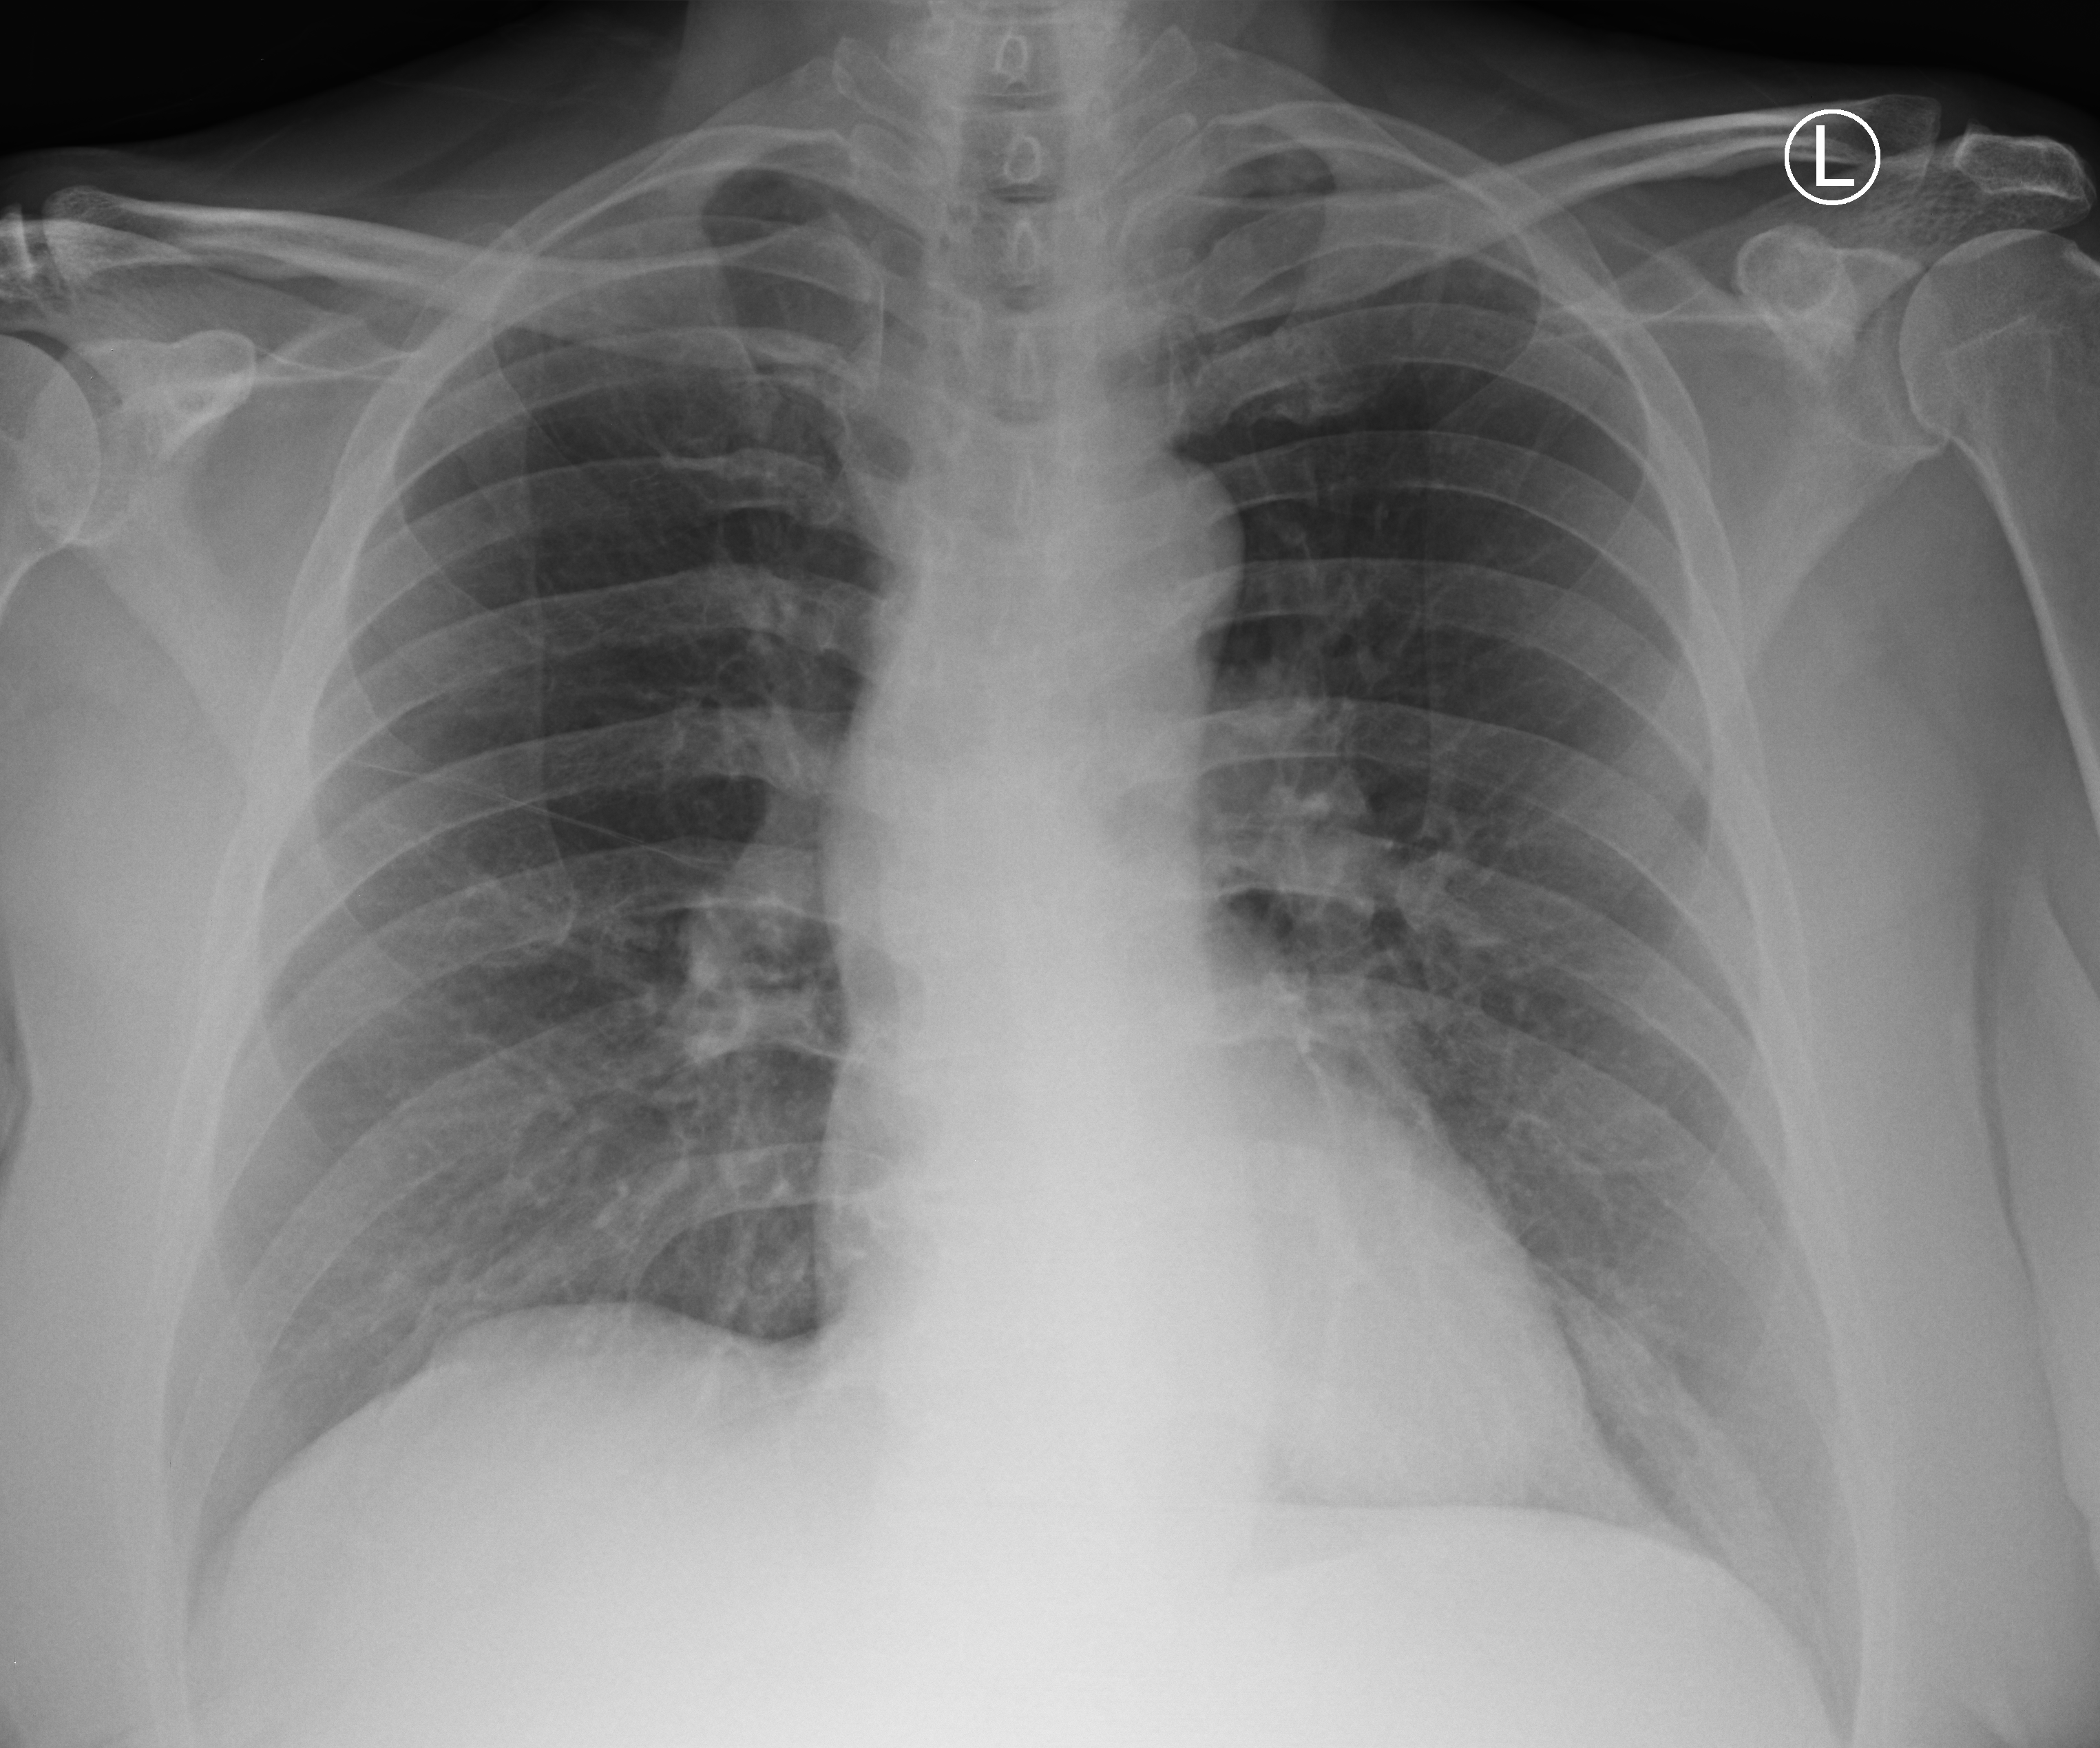
Portable chest radiograph; anteroposterior (AP) projection. Patient hospitalised with COVID-19; male, aged 60–74 years.
Admission-level facts for this patient (not findings on this image; timing relative to this image not recorded): chronic kidney disease (admission record): no; smoking status (admission record): former.